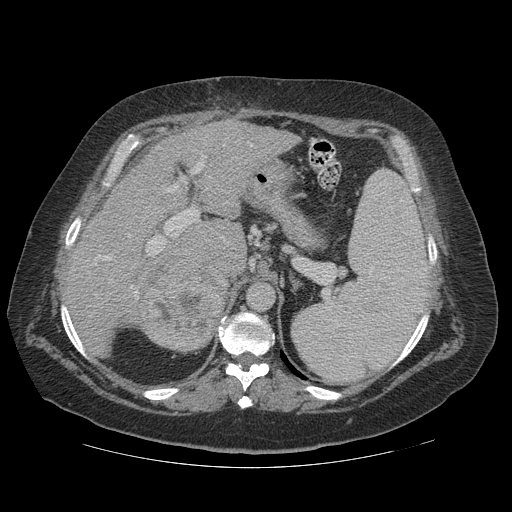
Contrast-enhanced abdominal CT (liver protocol), one axial slice. Position 78 of 121 along the scan axis. Reconstruction kernel STANDARD. 140 kVp. Soft-tissue window (W 400 / L 40 HU). 2.5 mm slice thickness. 512 × 512 image matrix. Case-level facts recorded for this patient, not image findings: diagnosis: hepatocellular carcinoma (patient treated with transarterial chemoembolisation; whether this scan precedes or follows treatment is not stated here); TNM stage (as recorded): Stage-IIIA; Child-Pugh class: A; tumour differentiation: well differentiated; tumour nodularity: multinodular.
Outlined on this slice (semi-automatic segmentation, software-assisted and operator-edited):
- liver parenchyma outside the tumour (the mass and vessels are separate outlines, so this box may not span the whole liver): box from (x=64, y=120) to (x=299, y=352) px
- mass: (x=133, y=250)–(x=230, y=352)
- liver vessels: (x=75, y=141)–(x=253, y=299)